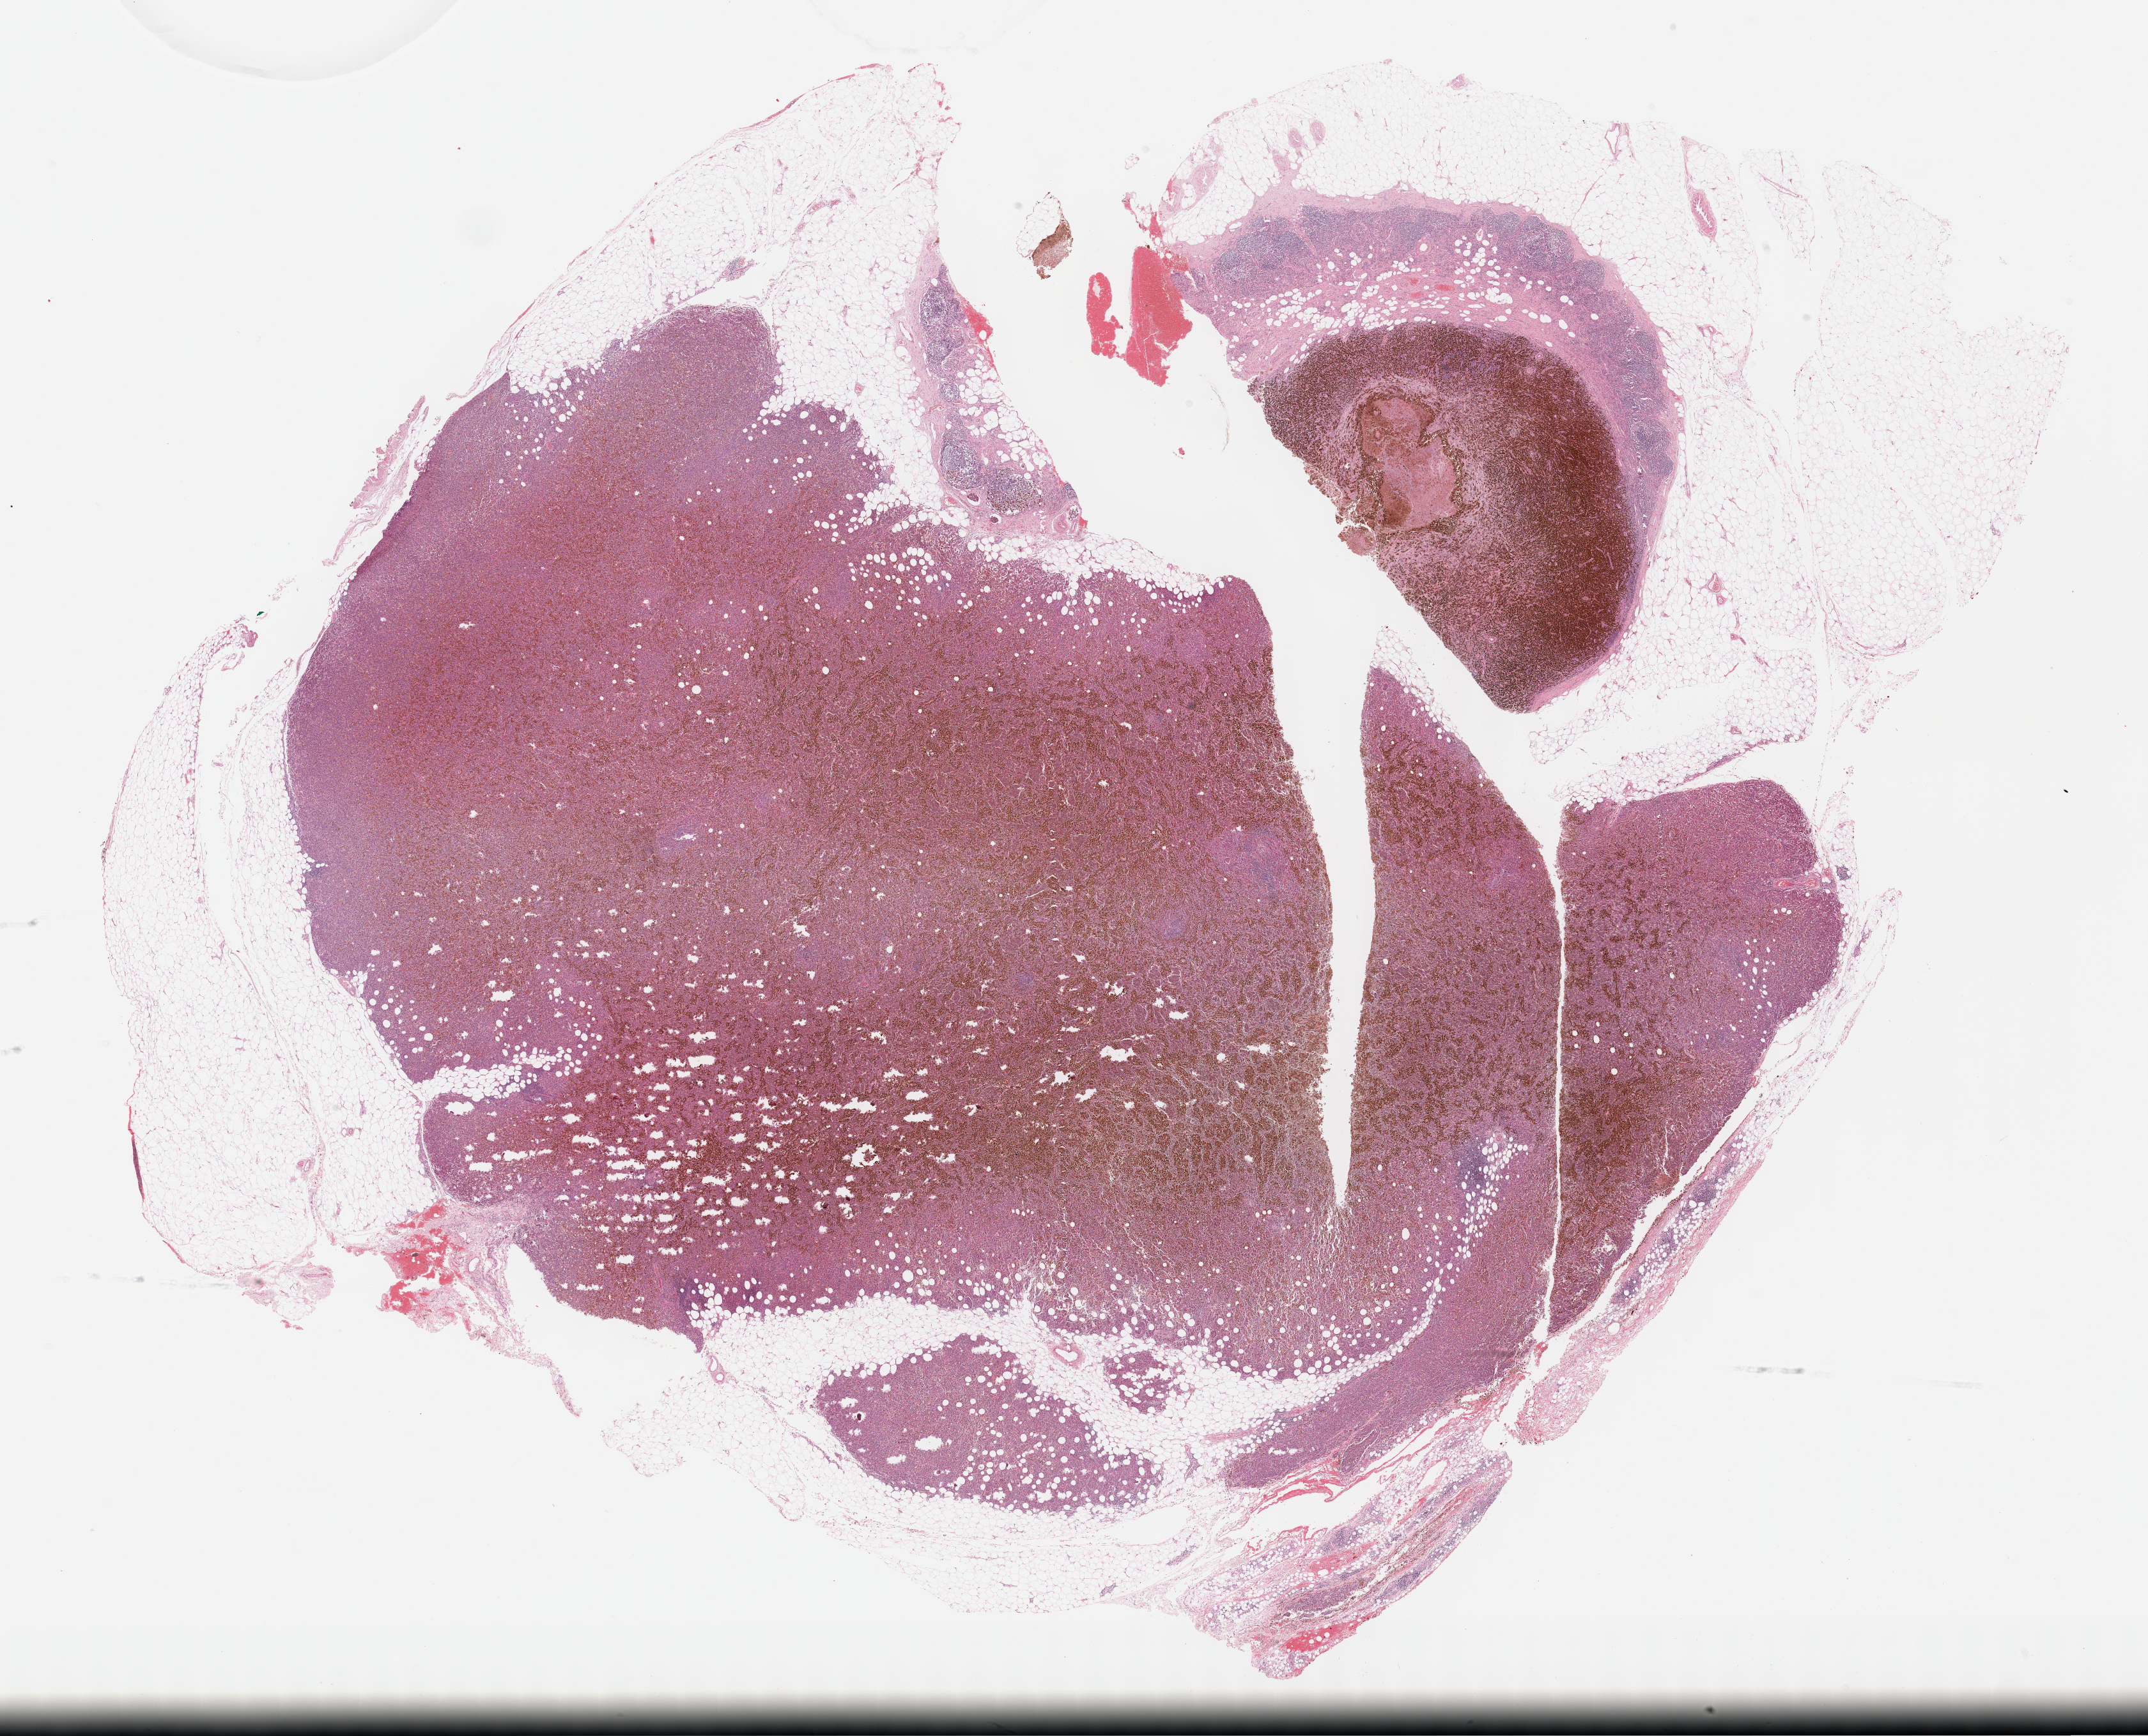
Hematoxylin and eosin (H&E) stained whole-slide image — whole scanned area (about 27.2 x 22.0 mm, slide scanned at 40x) shown as a low-resolution overview. Formalin-fixed paraffin-embedded (FFPE) diagnostic section. Metastatic tumour sample. Male, age 57 years at initial diagnosis.
- this section: metastatic tumour tissue
- patient diagnosis: Malignant melanoma, NOS